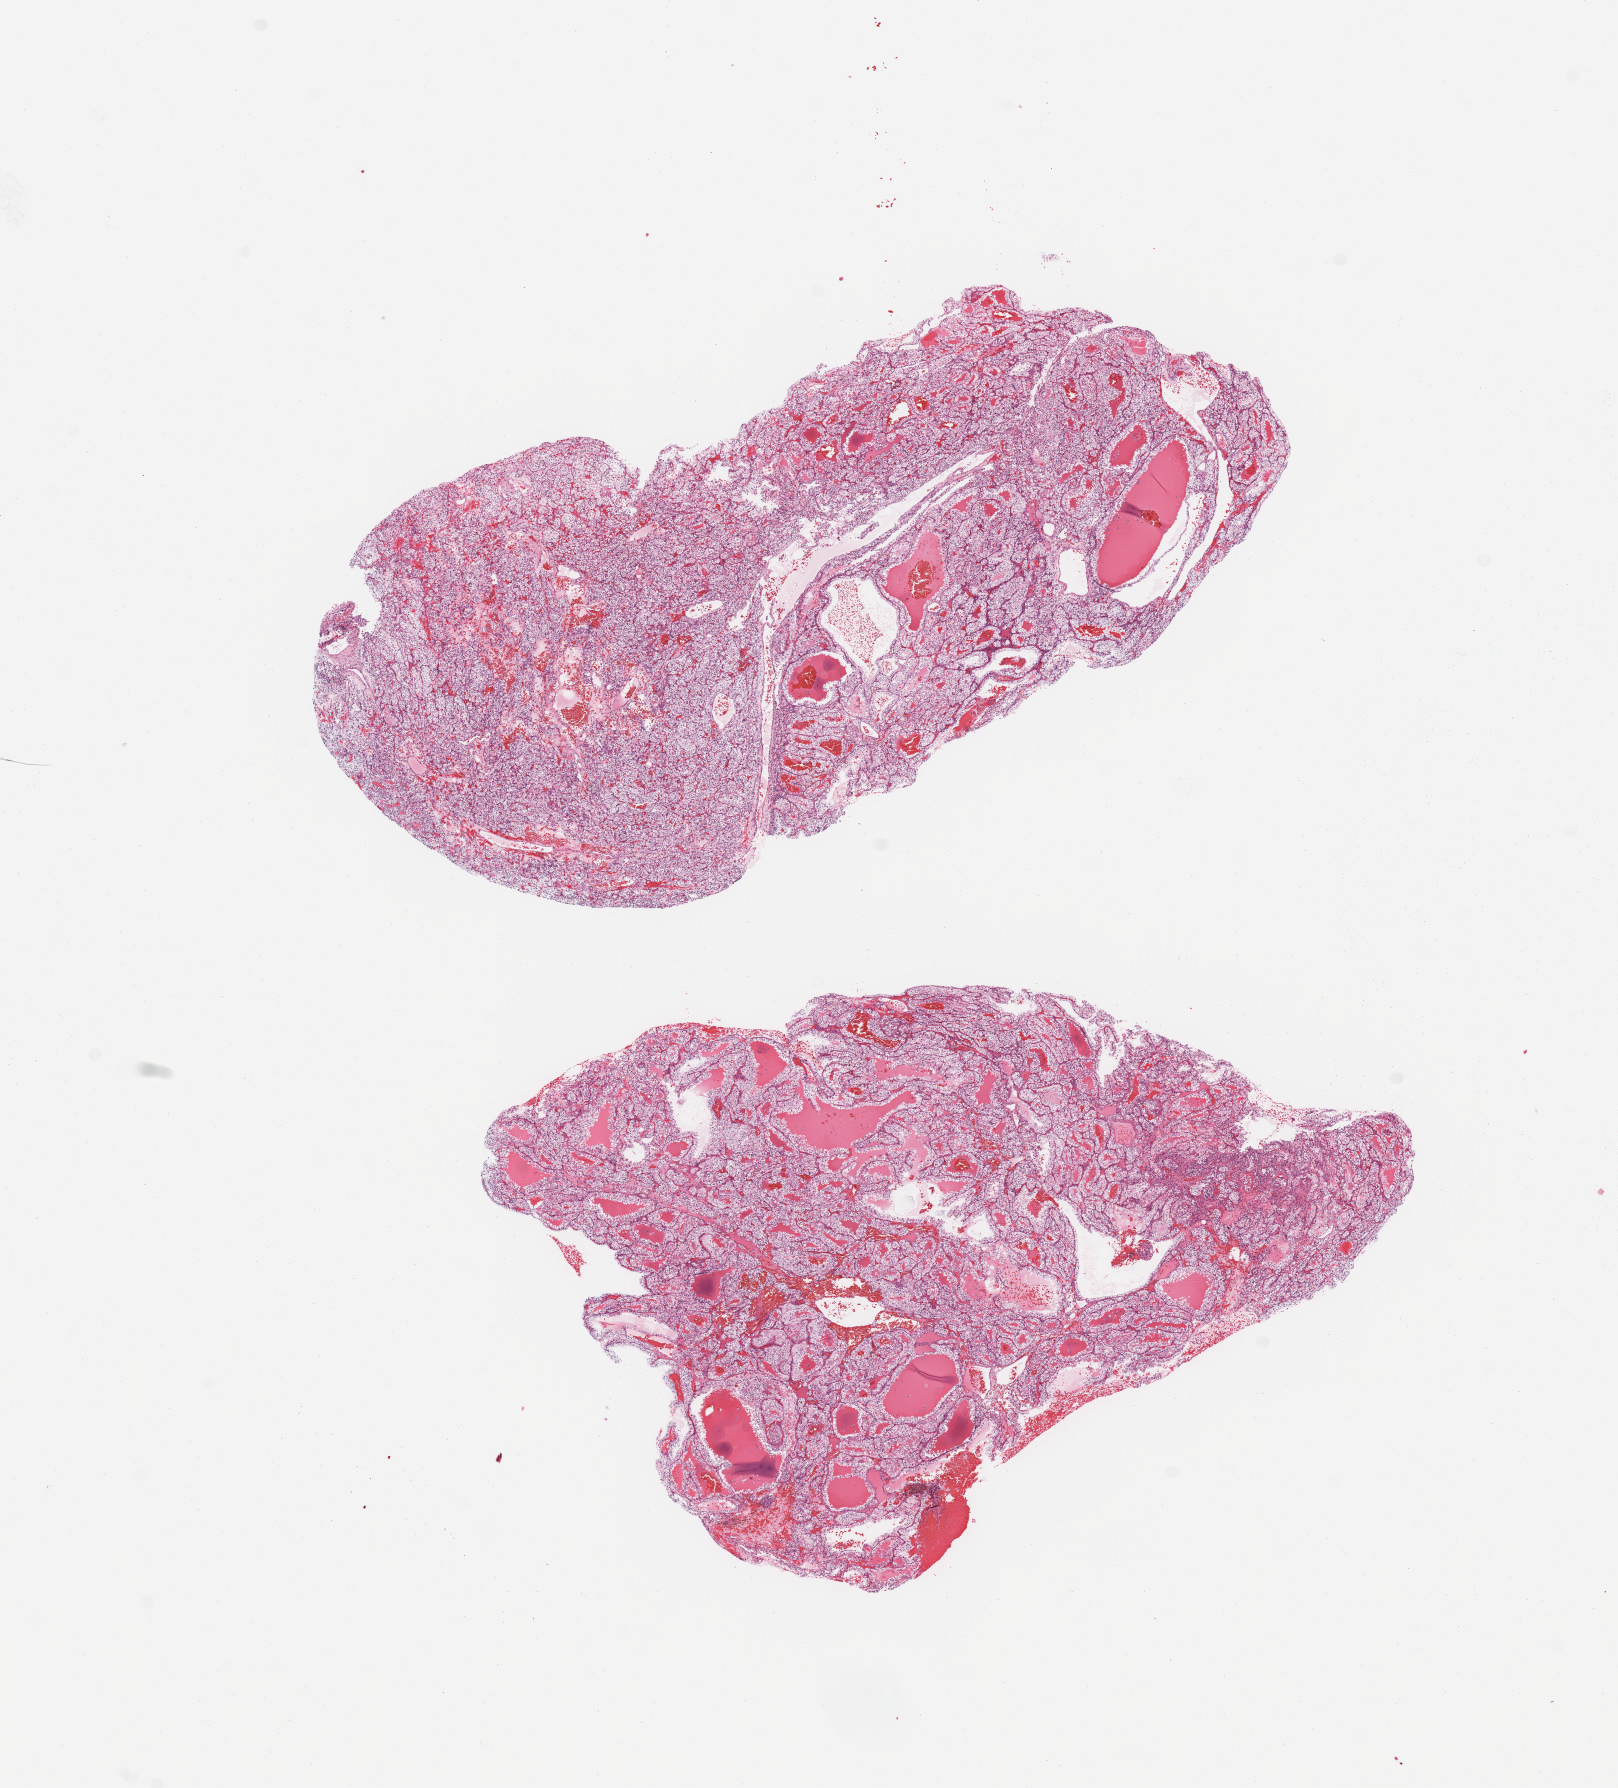
H&E-stained whole-slide image, whole scanned area (about 12.8 x 14.1 mm, from a 20x scan) shown as a low-resolution overview; tumour tissue sample, sampled site: kidney. 63-year-old male patient. Pathologist review of this section (percent, as recorded): tumour nuclei 85%, necrosis 0%.
Diagnosis: Renal cell carcinoma, NOS.